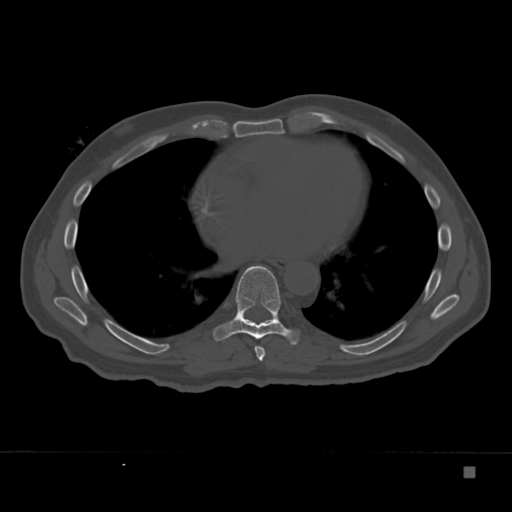
CT including the spine, one axial slice; slice 208 of 332 in the series (ordered by position); 120 kVp; bone window (W 1800 / L 400 HU); 1.5 mm slice thickness; 512 × 512 image matrix. Male patient, age 72 years. From the clinical record (not read from this slice): primary cancer: skeletal.
Structures marked on this image (semi-automatic segmentation, software-assisted and operator-edited):
- T7 vertebra: bounding box [x1, y1, x2, y2] px = [254, 346, 266, 361]
- T8 vertebra: [213, 265, 299, 345]